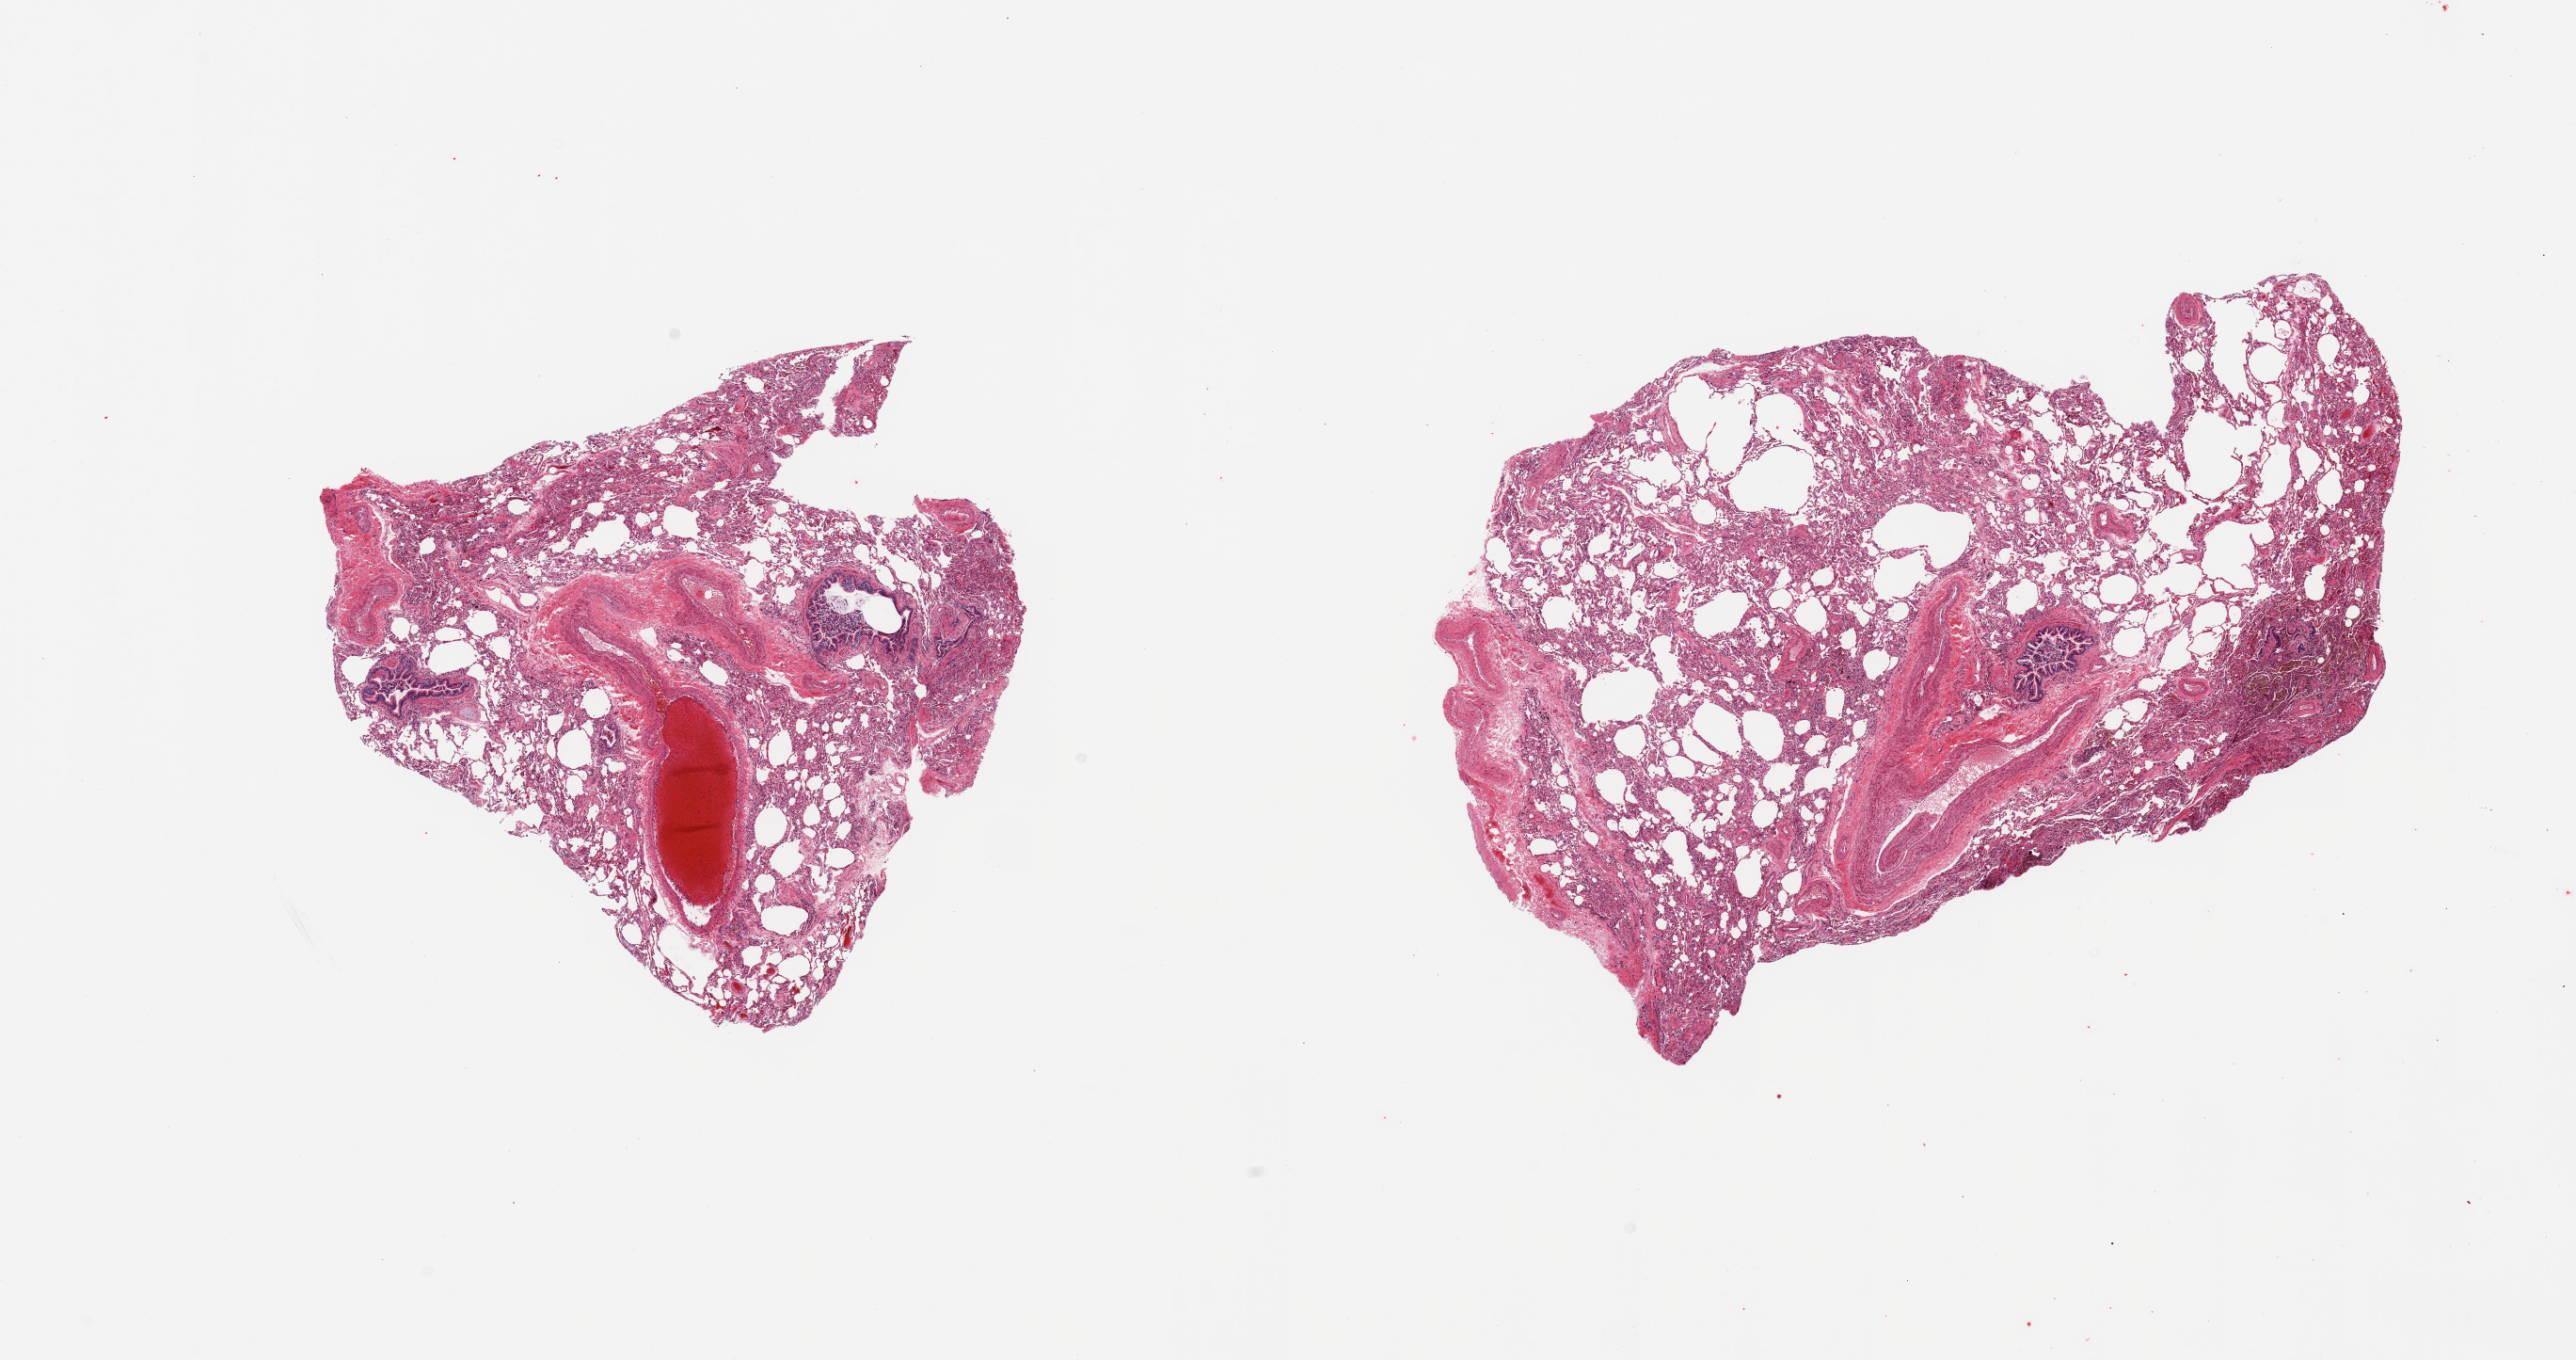
Whole-slide image, haematoxylin and eosin stain — shown as a low-resolution overview of the whole scanned area (about 21.7 x 11.4 mm); PAXgene-fixed paraffin-embedded (PFPE) section; section of lung (target tissue); tissue donor sample. Donor sex: male.
Review note (as recorded): 2 pieces, moderate chronic congestion/atalectasis; well fixed/defined bronchial mucosa.